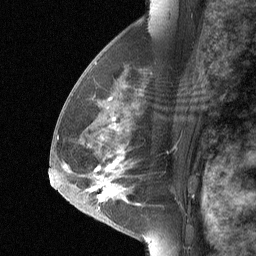
Breast MRI (dynamic contrast-enhanced), one sagittal slice; slice 36 of 64 in the series (ordered by position); dynamic contrast-enhanced study with each time point stored as its own series, time point 2 of 3 at this slice position (early post-contrast, ordered by acquisition time); 1.5 T; TE 4.8 ms, TR 27 ms; 2 mm slice thickness; 256 × 256 image matrix. Patient: female, 56 years. From the clinical record (not read from this slice): setting: breast cancer imaged before/during neoadjuvant chemotherapy; receptor status: HER2-positive.
Outlined on this slice (semi-automatic segmentation, software-assisted and operator-edited):
- analysis volume of interest (the breast-tissue region the enhancement analysis was run in; not a lesion): bounding box [x1, y1, x2, y2] px = [68, 83, 146, 214]
- tumour enhancement mask (voxels above the 90 % enhancement threshold inside the analysis volume of interest): [91, 119, 118, 201]